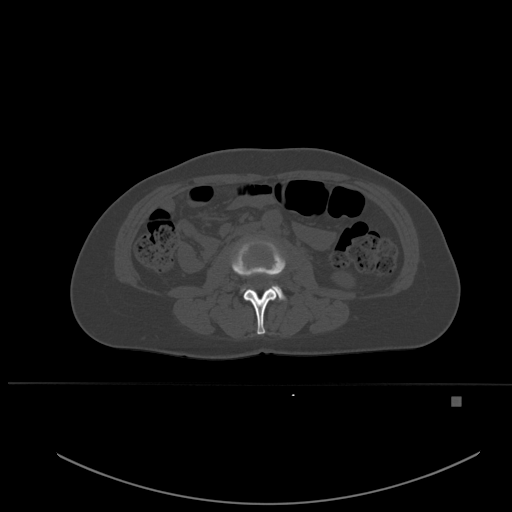
CT including the spine, one axial slice; position 205 of 651 along the scan axis; bone window (W 1800 / L 400 HU); 1.5 mm slice thickness; 512 × 512 image matrix, field of view 443 × 443 mm. Patient: female, 49 years. Case-level facts recorded for this patient, not image findings: primary cancer: breast; vertebrae with lytic lesions (as recorded): L3, T12, L4.
Annotated regions visible in this slice (semi-automatic segmentation, software-assisted and operator-edited):
- L2 vertebra: bounding box [x1, y1, x2, y2] px = [231, 239, 286, 335]
- L3 vertebra: [244, 285, 285, 300]